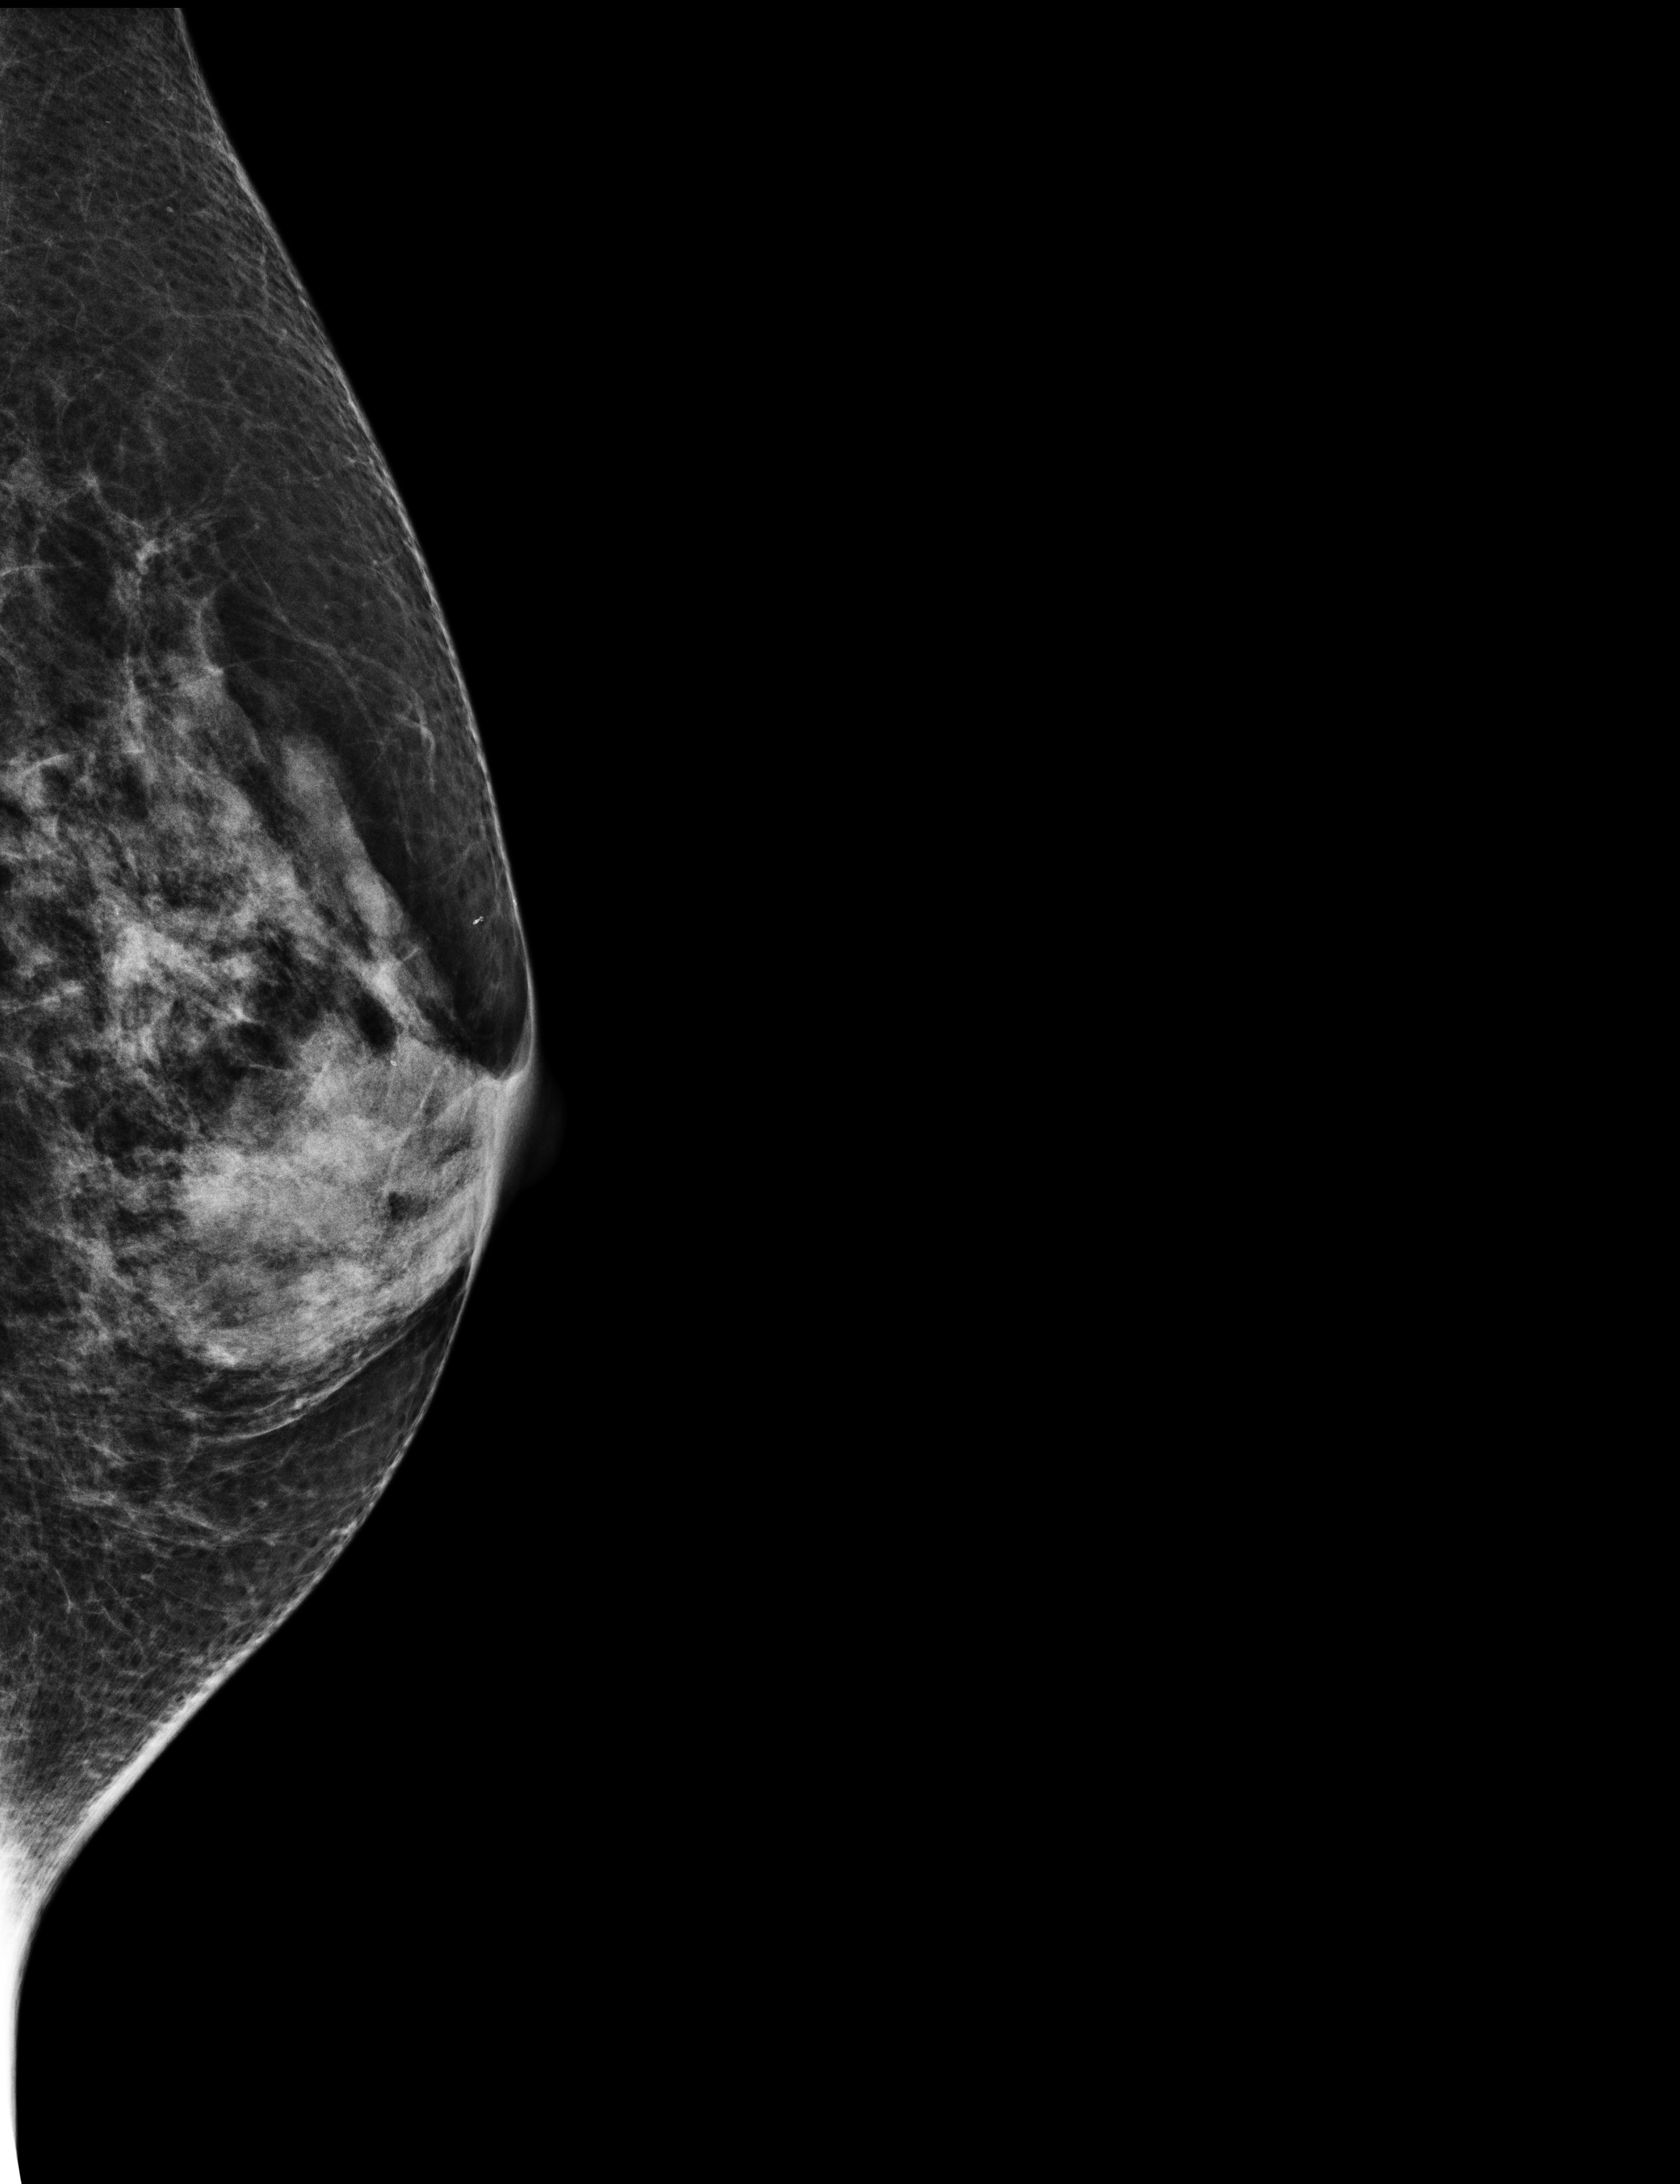
Digital mammogram (FFDM), left breast, mediolateral (ML) view, annual screening mammography examination, compressed breast thickness 42 mm. Female patient, age 59 years.
- BI-RADS breast density category at the screening exam (both breasts, scale 1–4): 3
- final BI-RADS assessment for this screening round (tomosynthesis exam, both breasts): category 1
- recall: no recall after this screen